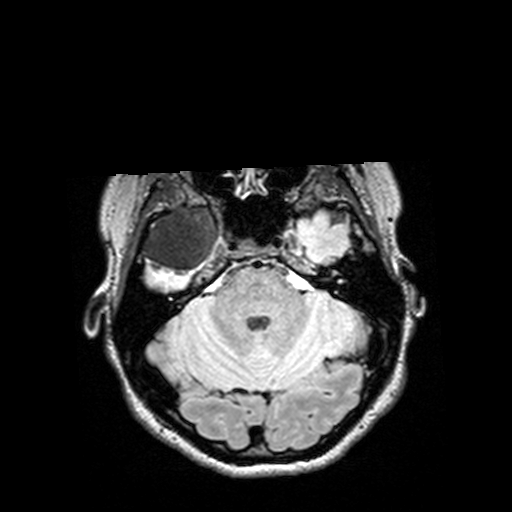
Brain MRI from a brain-tumour surgery series, one axial slice. T2 FLAIR. 1 mm slice thickness. 512 × 512 image matrix. Case-level facts recorded for this patient, not image findings: histopathology: Astrocytoma; WHO grade: 3.
Outlined on this slice (outlined manually by an expert reader):
- tumour: bounding box [x1, y1, x2, y2] px = [126, 205, 232, 275]